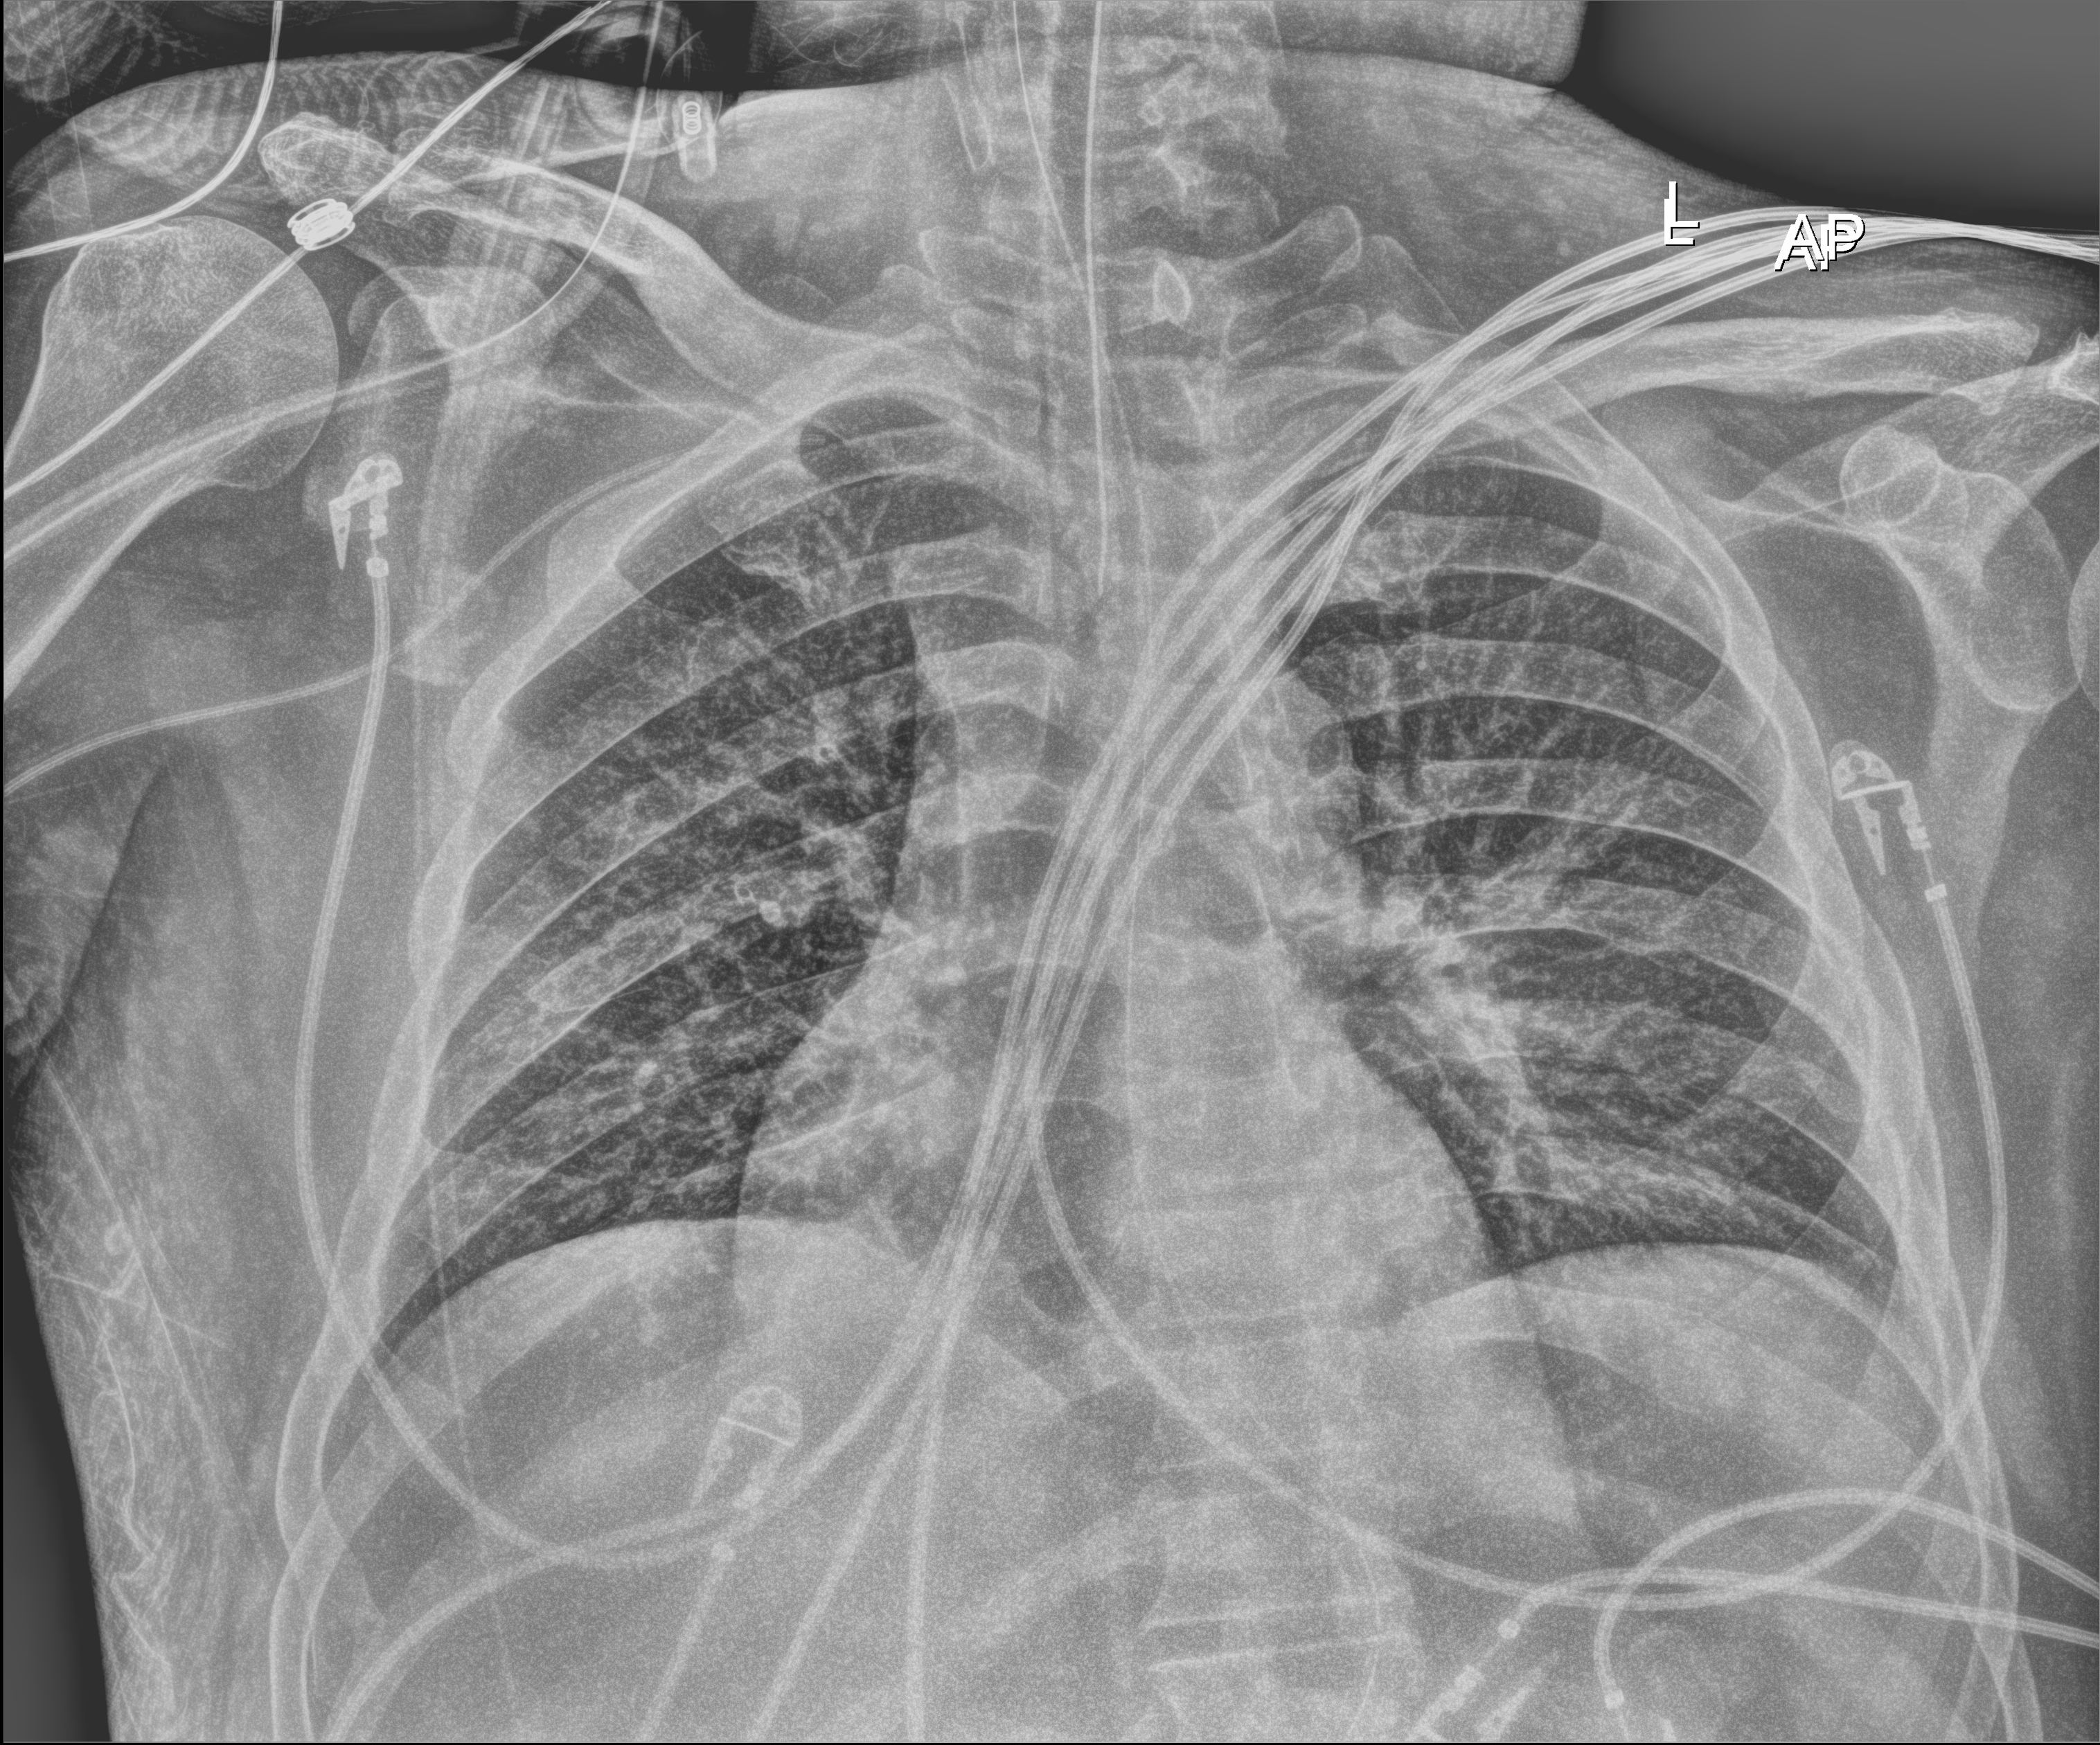
Bedside chest radiograph (digital radiography), anteroposterior (AP) projection. Patient hospitalised with COVID-19; male, aged 18–59 years.
From the hospital-stay record, not from the radiograph (when in the stay this image was taken is not recorded):
- mechanically ventilated during this hospital stay: yes
- admitted to intensive care during this hospital stay: yes